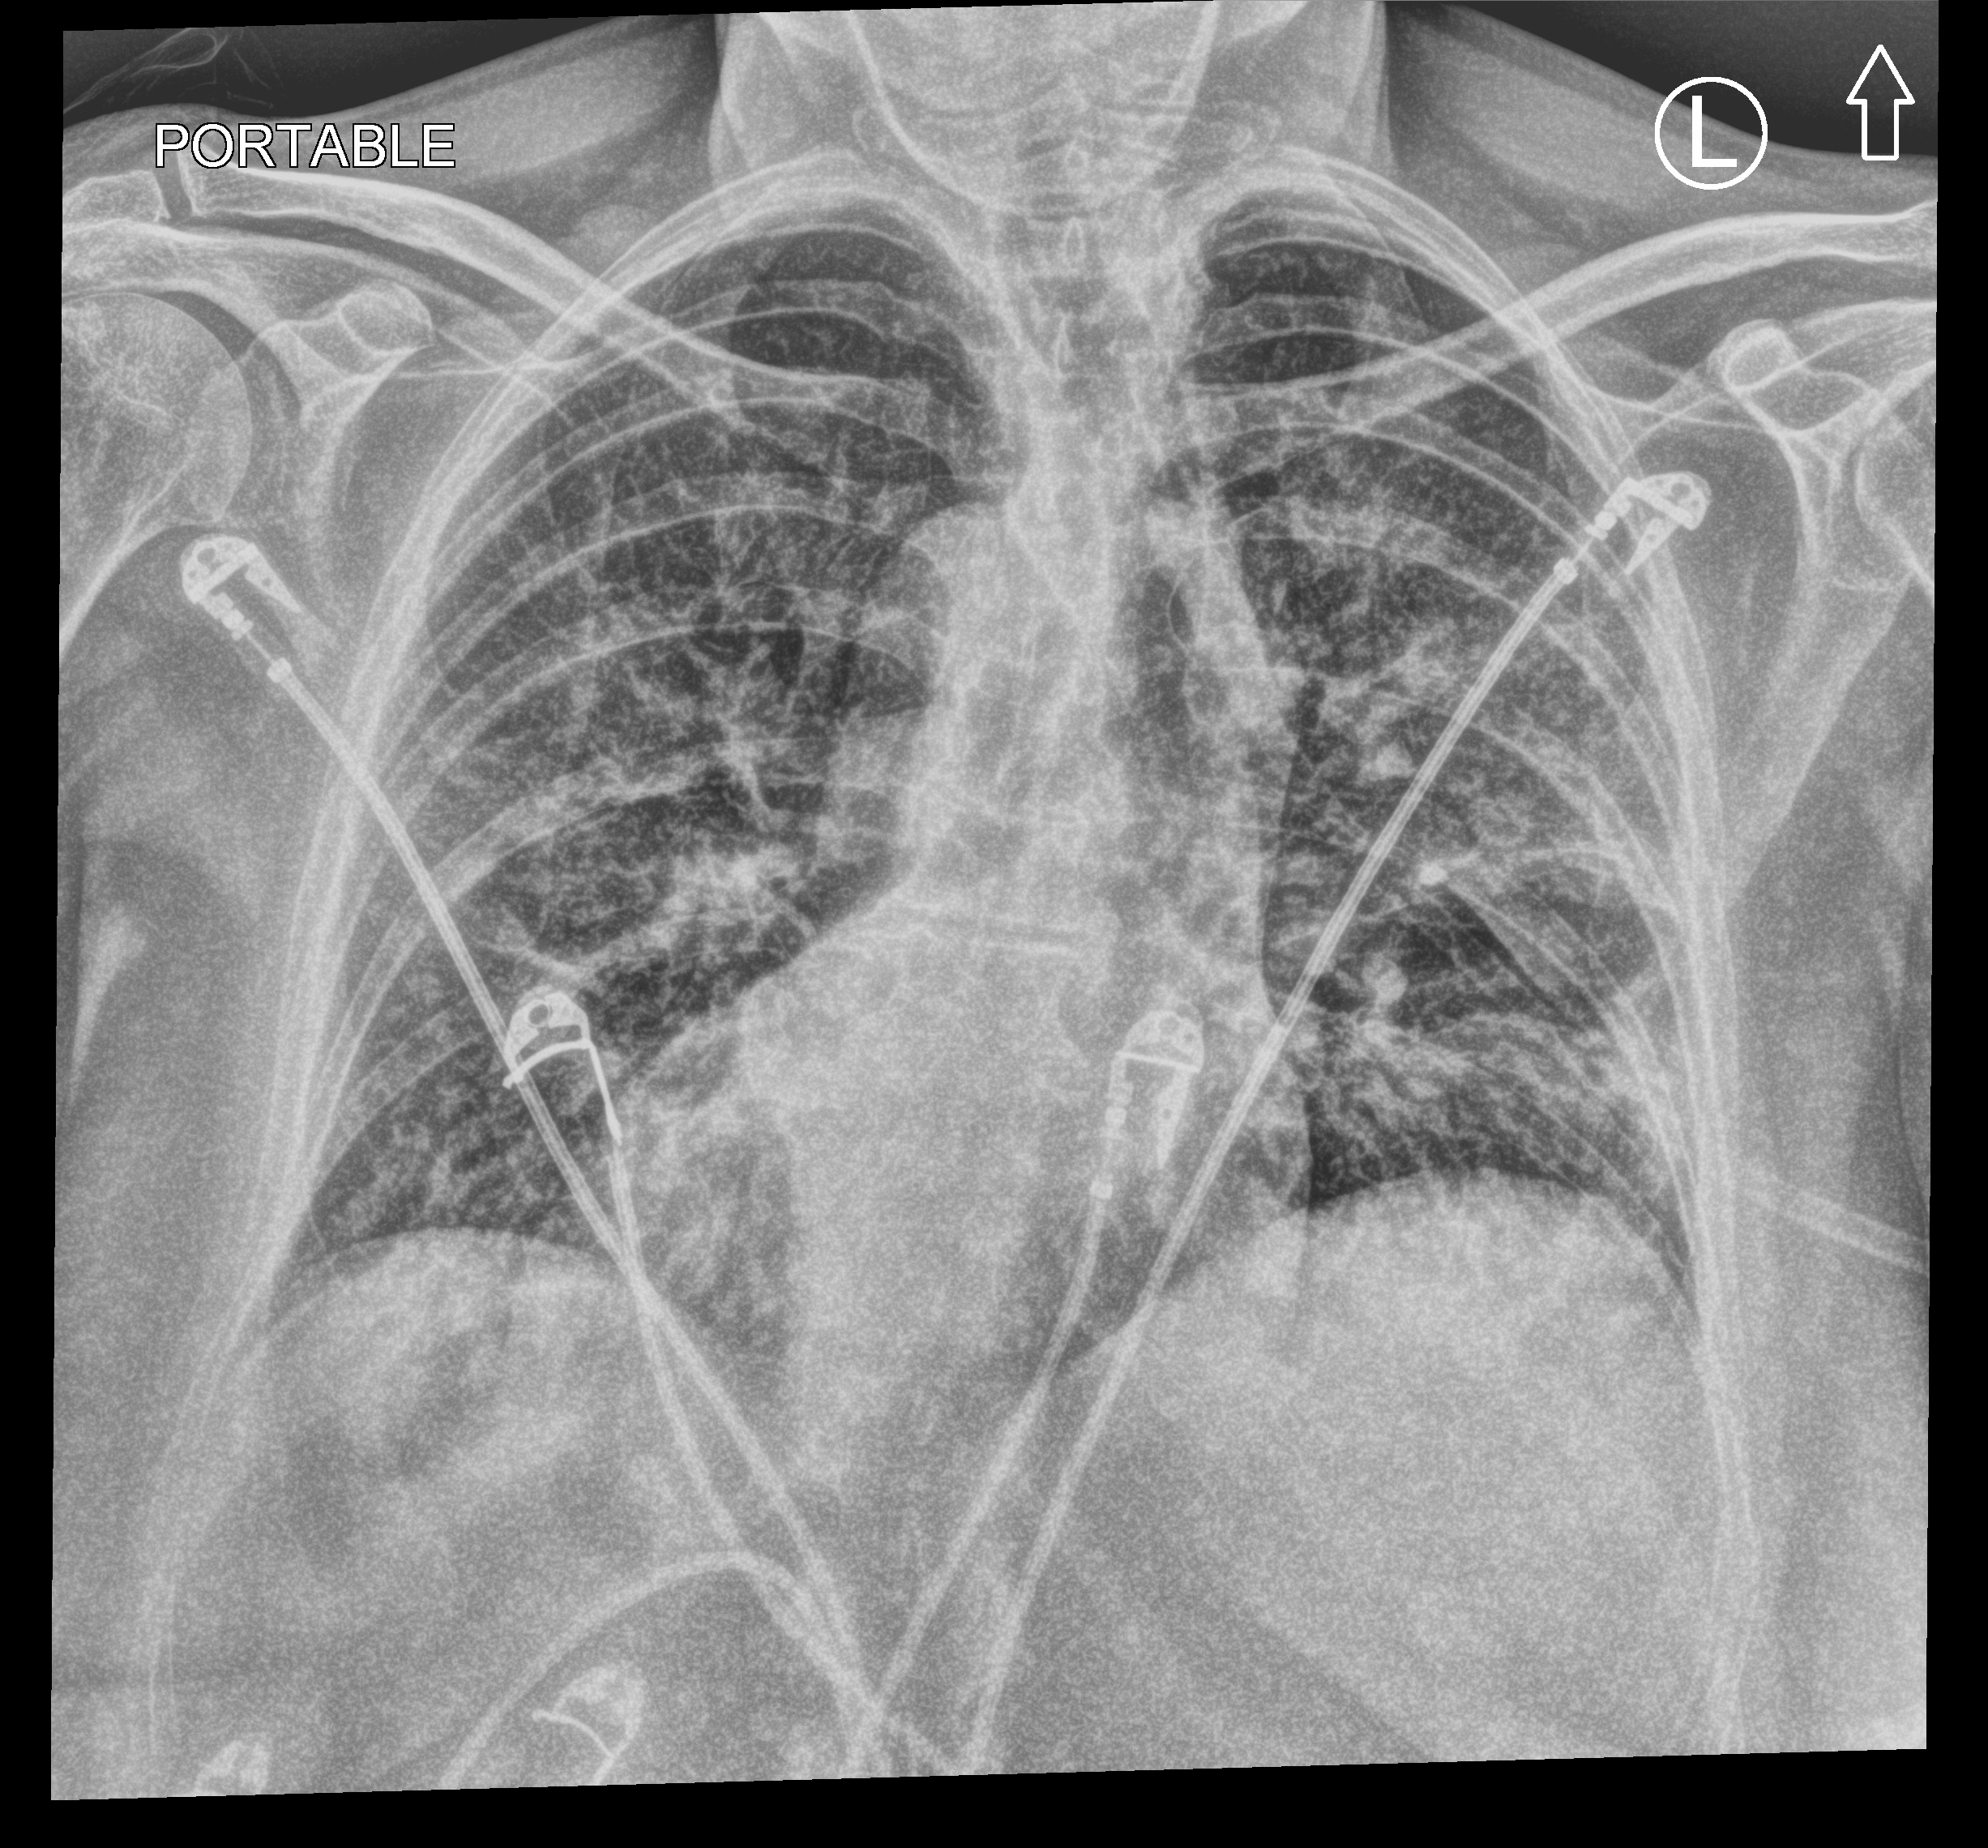
Chest X-ray (portable). Patient hospitalised with COVID-19; female, aged 60–74 years.
From the hospital-stay record, not from the radiograph (when in the stay this image was taken is not recorded):
- hypertension (admission record): yes